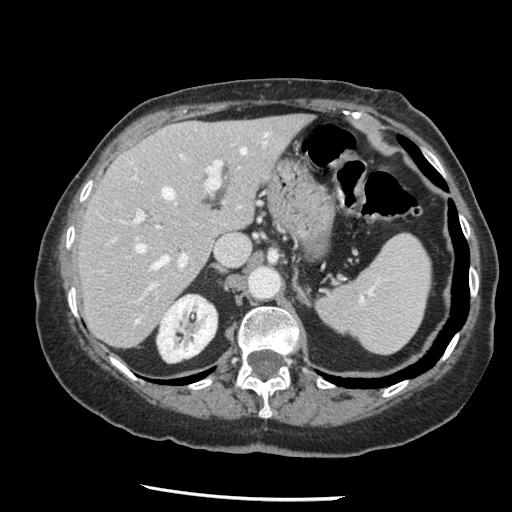
Contrast-enhanced abdominal CT, one axial slice. Slice 90 of 148 in the series (ordered by position). Soft-tissue window (W 400 / L 40 HU). 2.5 mm slice thickness. 512 × 512 image matrix, field of view 330 × 330 mm. Female patient, age 85 years. From the clinical record (not read from this slice): diagnosis: colorectal cancer liver metastases, imaged before liver resection; multiple liver metastases: no; largest metastasis: 0.9 cm.
Annotated regions visible in this slice (outlined manually by an expert reader):
- hepatic veins: bounding box (x1, y1, x2, y2) in pixels: (136, 134, 271, 269)
- liver: (79, 116, 309, 347)
- planned liver remnant (the part of the liver to remain after resection): (79, 116, 309, 347)
- portal vein (with intrahepatic branches): (113, 158, 223, 289)